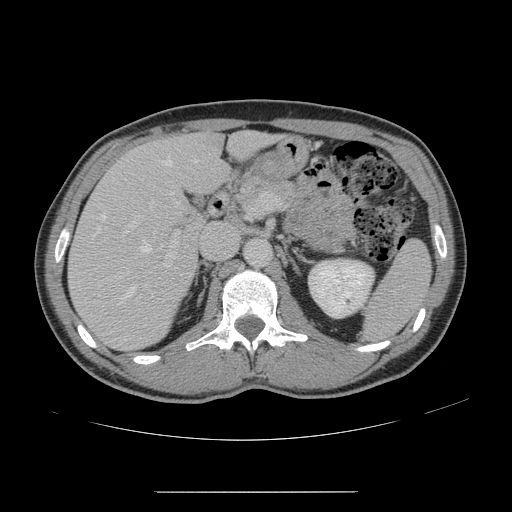
Contrast-enhanced abdominal CT, one axial slice; position 84 of 178 along the scan axis; intravenous contrast given; soft-tissue window (W 400 / L 40 HU); 2.5 mm slice thickness; 512 × 512 image matrix. Male patient, age 53 years. From the clinical record (not read from this slice): diagnosis: colorectal cancer liver metastases, imaged before liver resection; multiple liver metastases: yes; largest metastasis: 2.4 cm; disease in both lobes: no.
Structures marked on this image (manually delineated by an expert):
- hepatic veins: bounding box <94,159,197,306> (left, top, right, bottom; pixels)
- liver: <69,132,273,350>
- planned liver remnant (the part of the liver to remain after resection): <154,133,273,193>
- portal vein (with intrahepatic branches): <128,192,267,268>